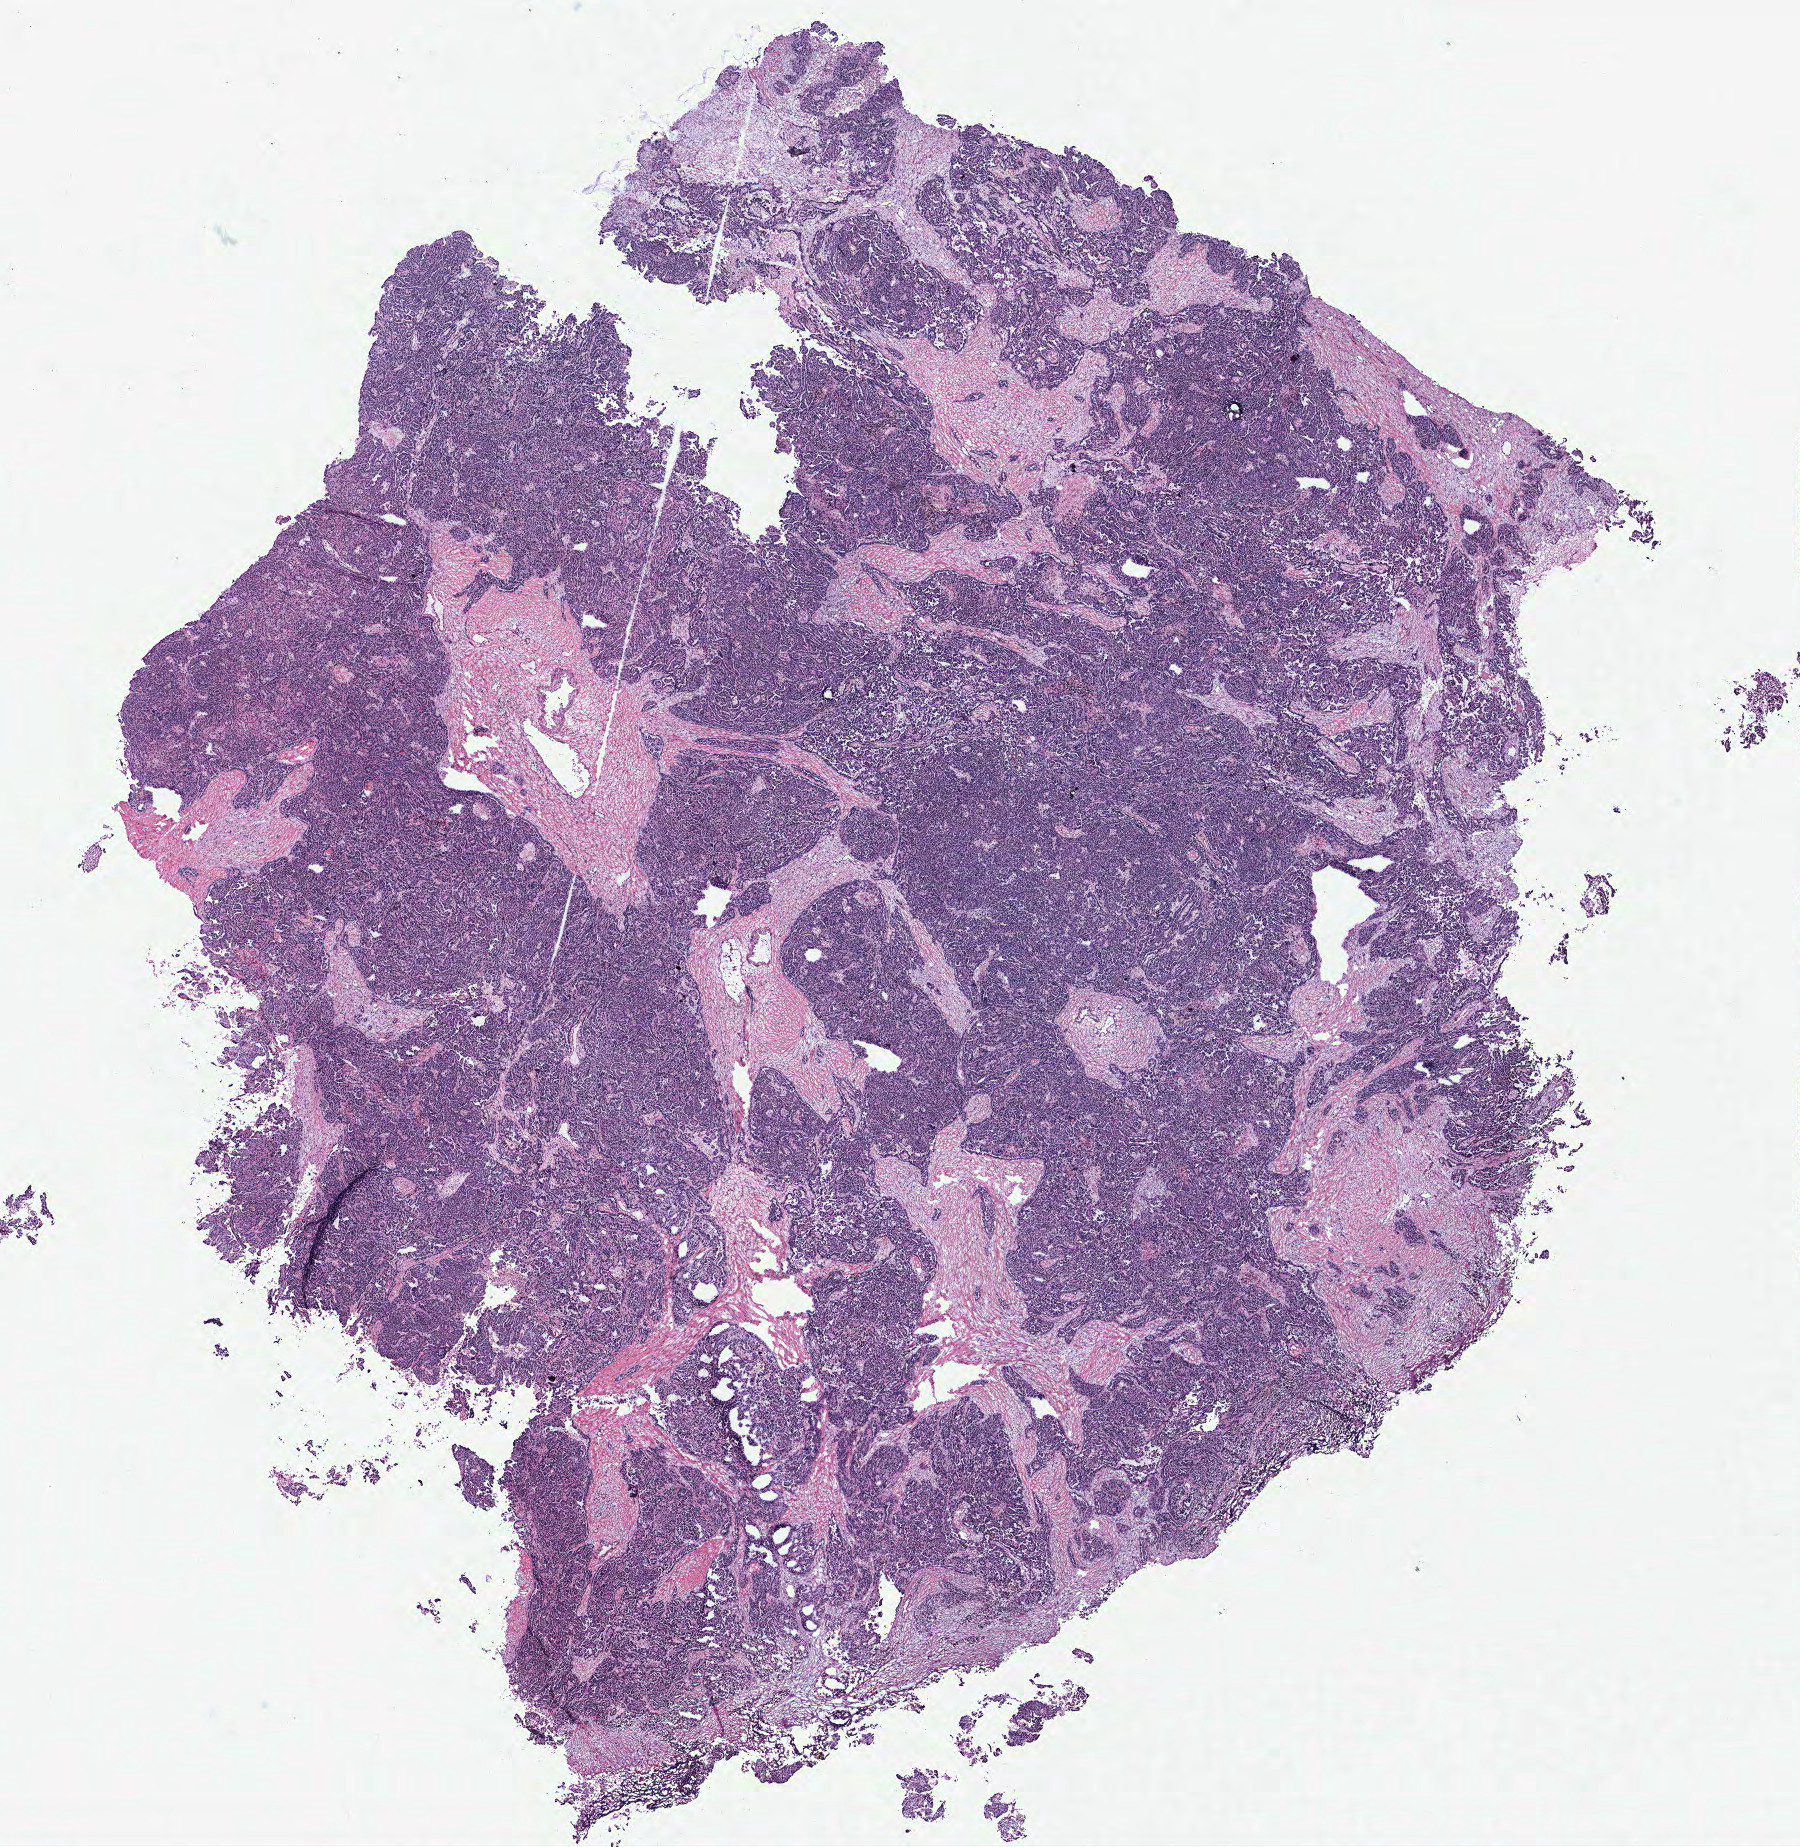
Whole-slide histology image, Hematoxylin and eosin (H&E) stained, whole scanned area (about 14.4 x 14.8 mm) shown as a low-resolution overview; ovary, tumour tissue. Patient: female, age 65 years.
• primary tumour site (as recorded): ovary
• histologic diagnosis: Serous adenocarcinoma, NOS